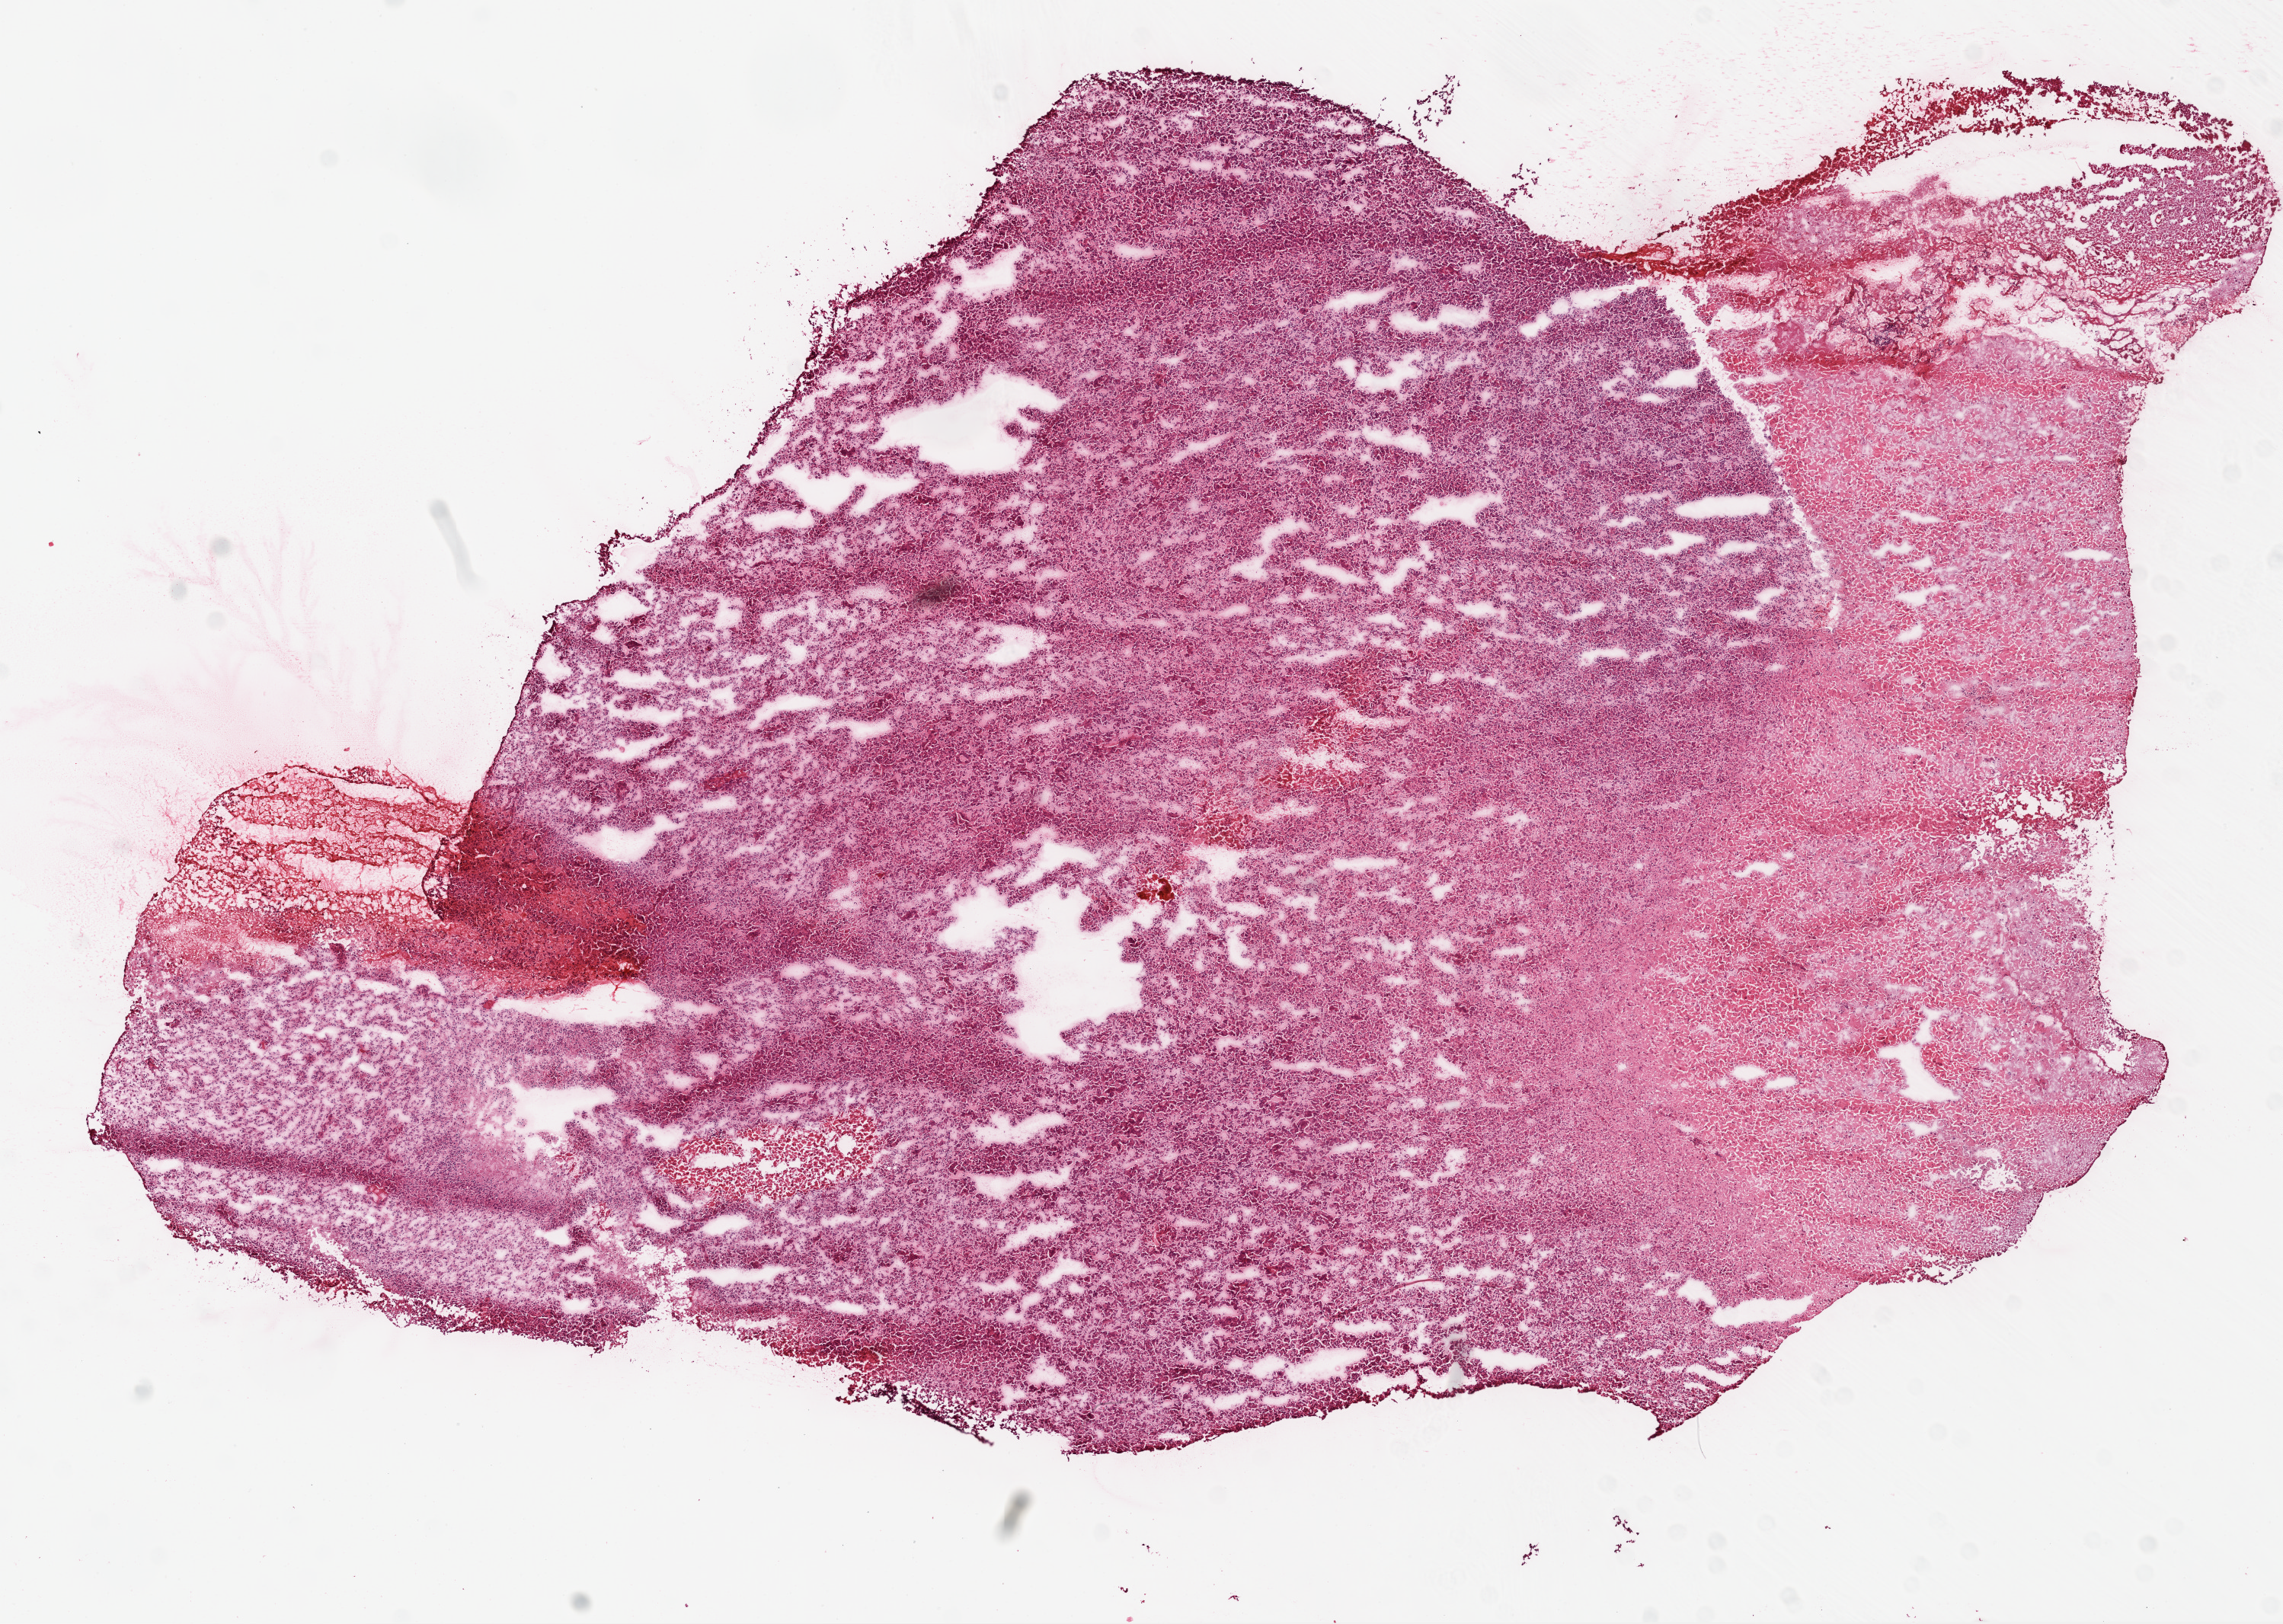
Digitized H&E-stained tissue section (whole slide) — a low-resolution overview of the entire scanned area, about 12.1 x 8.6 mm (from a 20x scan); frozen section; sample: primary tumour, brain. Female patient; age at initial diagnosis 51 years. Pathologist review of this section (percent, as recorded): tumour cells 70%, tumour nuclei 100%, normal cells 0%, stromal cells 0%, necrosis 30%.
• histologic diagnosis: Glioblastoma